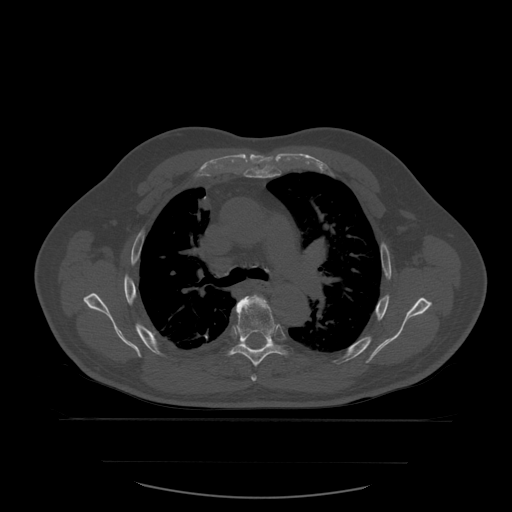
CT including the spine, one axial slice. Position 407 of 590 along the scan axis. Bone window (W 1800 / L 400 HU). 512 × 512 image matrix. Patient age 71 years. Case-level facts recorded for this patient, not image findings: primary cancer: lung; vertebrae with lytic lesions (as recorded): T1, T2, L5, S1.
Outlined on this slice (semi-automatically segmented with operator editing):
- T5 vertebra: bounding box (x1, y1, x2, y2) in pixels: (251, 295, 266, 382)
- T6 vertebra: (218, 296, 294, 369)